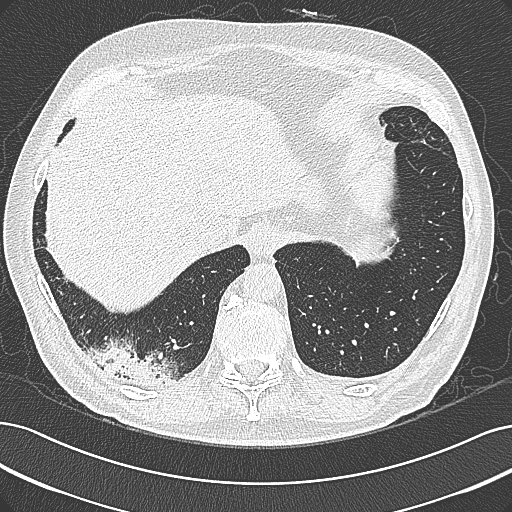
Low-dose screening chest CT, axial slice, first (baseline) screen, lung window (W 1500 / L -600 HU), 1 mm slice thickness, slice 243 of 355 in the series. Male, age 68 years at enrolment.
Expert-annotated lung lesion, bounding box [x1, y1, x2, y2] px = [96, 339, 190, 400]. No non-calcified nodule or mass ≥4 mm was recorded by the screening reader at this exam. Participant outcome: lung cancer diagnosed 154 days after this screen — mucinous adenocarcinoma, right lower lobe, well differentiated (G1), stage IB (AJCC 6th edition), 50 mm at pathology.